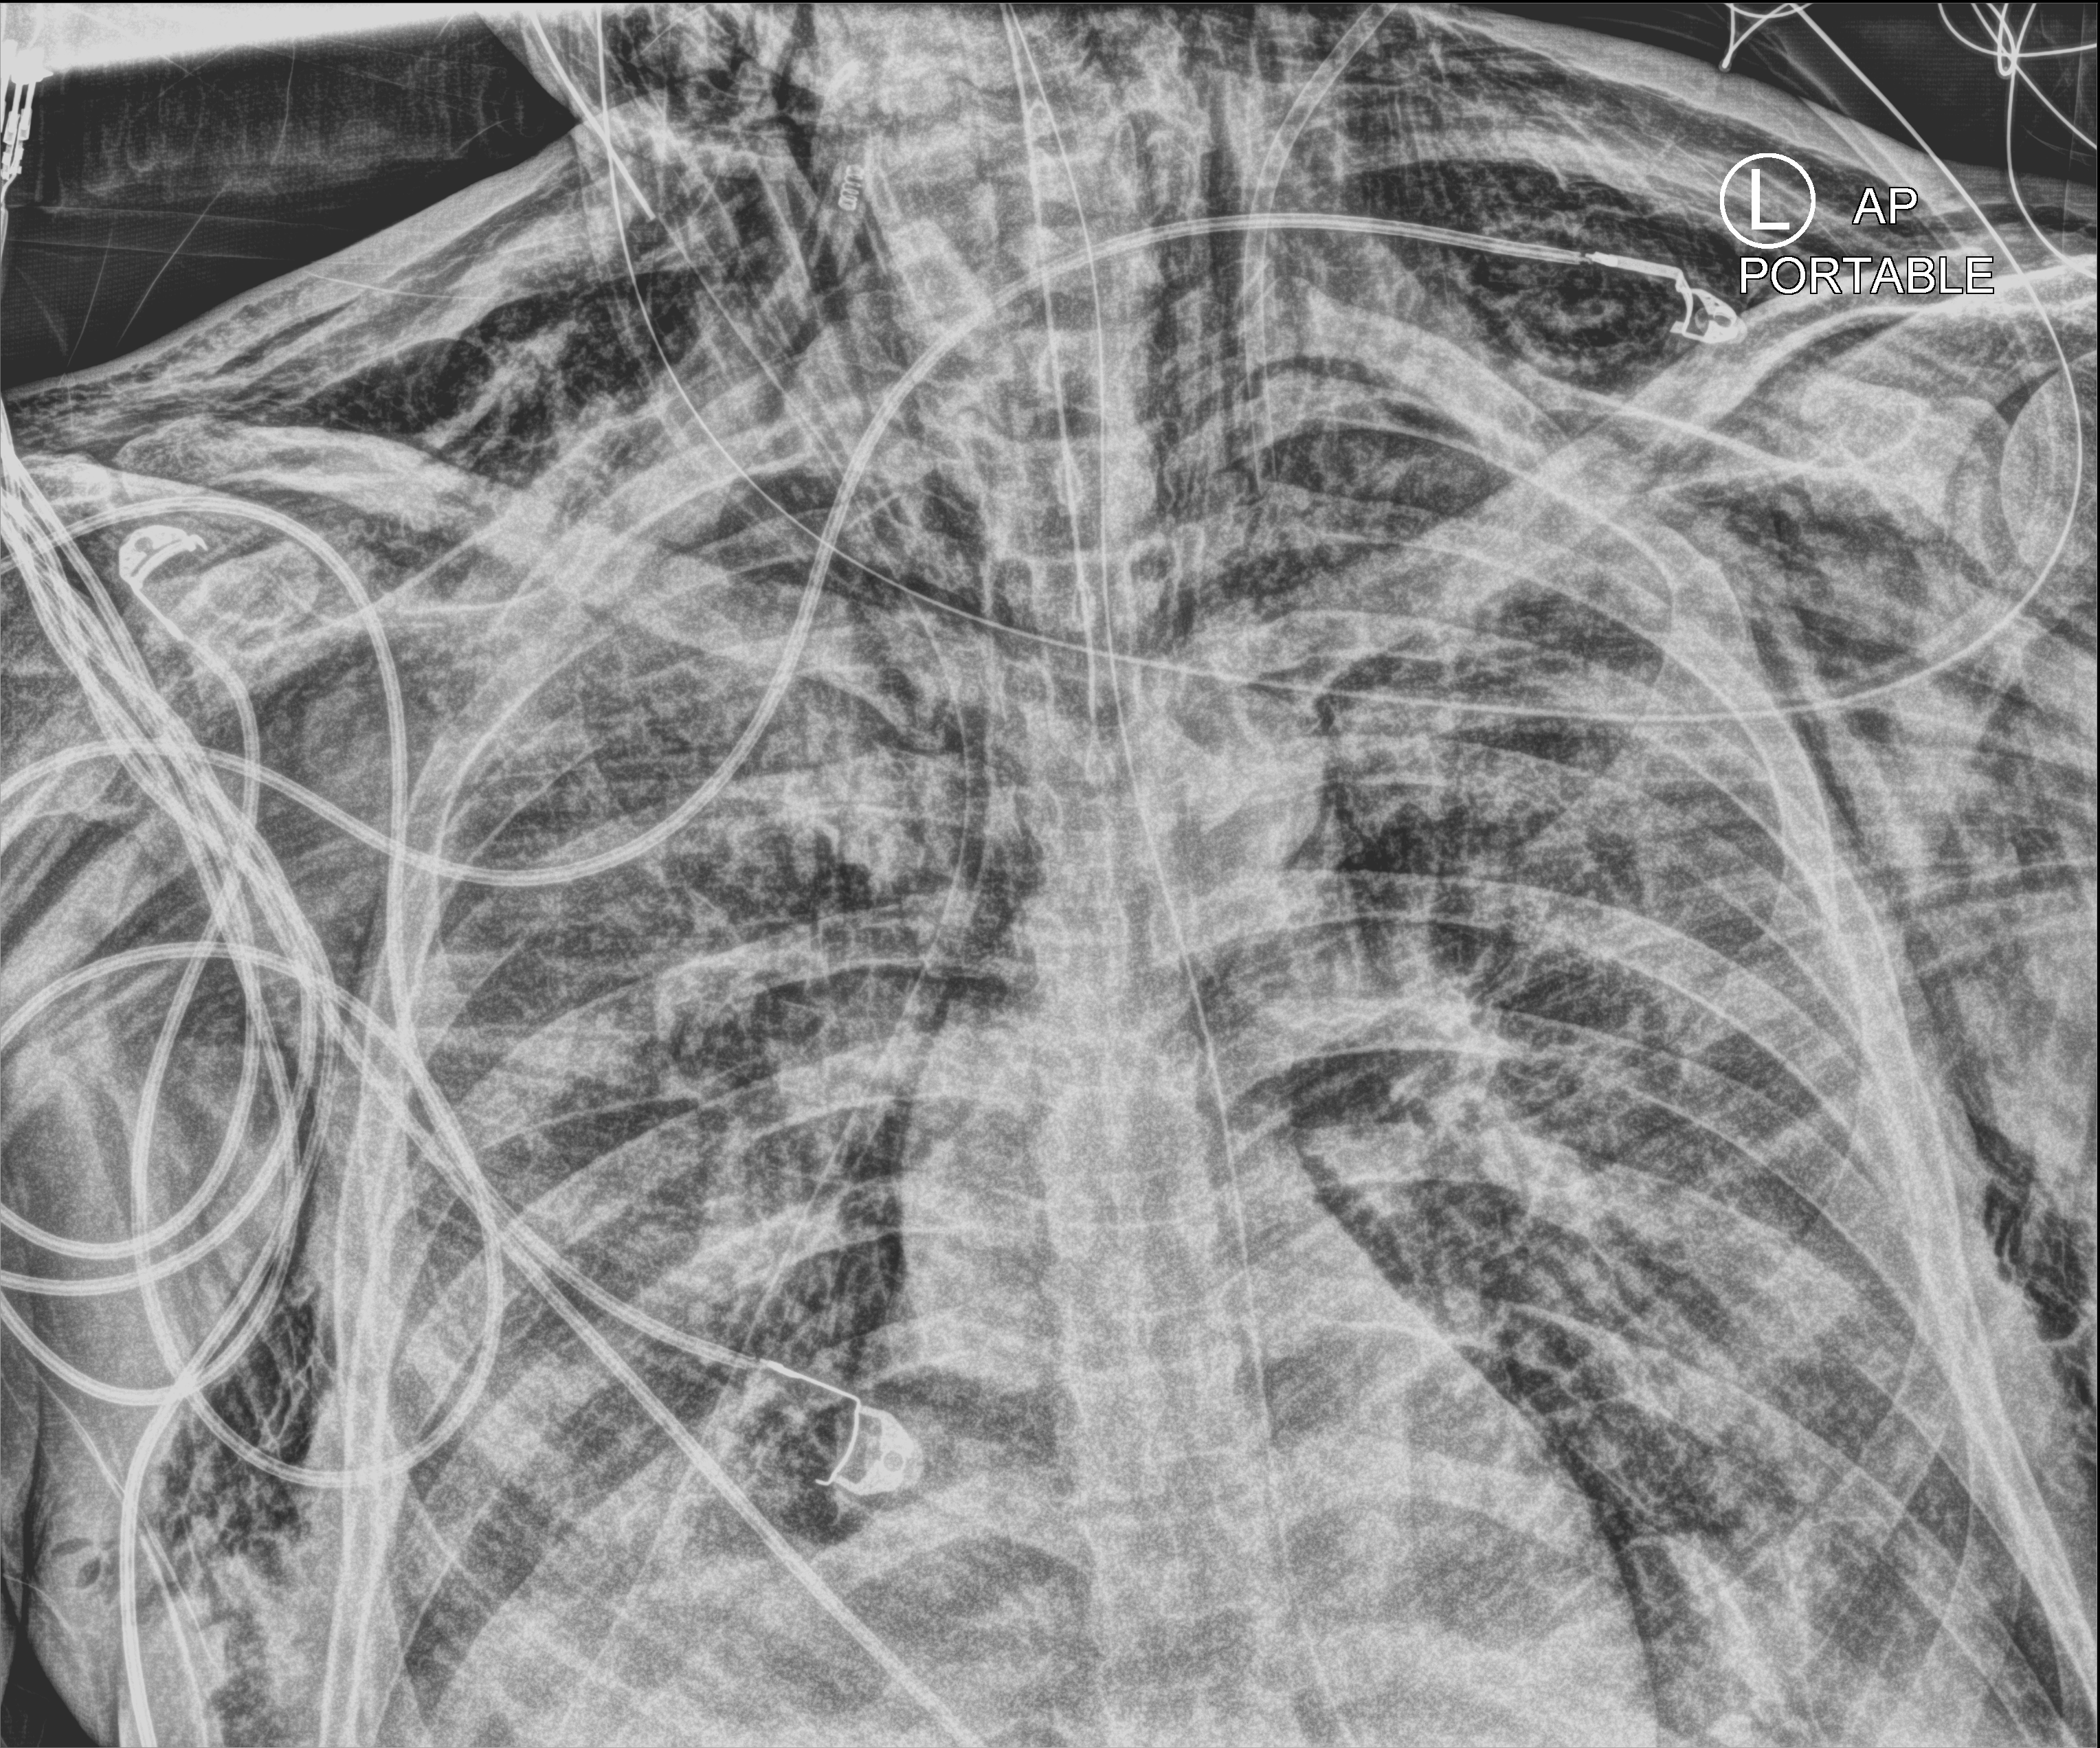
Chest X-ray (portable), anteroposterior (AP) projection. Patient hospitalised with COVID-19; male, aged 60–74 years.
Hospital-stay facts (about this admission, not read from this image; timing relative to this image not recorded):
- mechanically ventilated during this hospital stay: yes